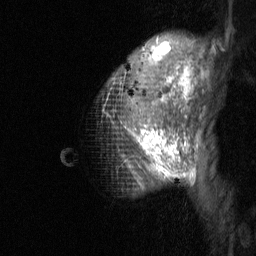
Breast MRI (dynamic contrast-enhanced), one sagittal slice; slice 49 of 64 in the series (ordered by position); dynamic contrast-enhanced study with each time point stored as its own series, time point 2 of 3 at this slice position (early post-contrast, ordered by acquisition time); 1.5 T; TE 4.8 ms, TR 27 ms; 2 mm slice thickness; 256 × 256 image matrix, field of view 180 × 180 mm. Female patient, age 36 years. From the clinical record (not read from this slice): setting: breast cancer imaged before/during neoadjuvant chemotherapy; receptor status: HR-positive, HER2-negative.
Annotated regions visible in this slice (semi-automatic segmentation, software-assisted and operator-edited):
- analysis volume of interest (the breast-tissue region the enhancement analysis was run in; not a lesion): bounding box <102,33,210,197> (left, top, right, bottom; pixels)
- tumour enhancement mask (voxels above the 90 % enhancement threshold inside the analysis volume of interest): <142,43,196,179>